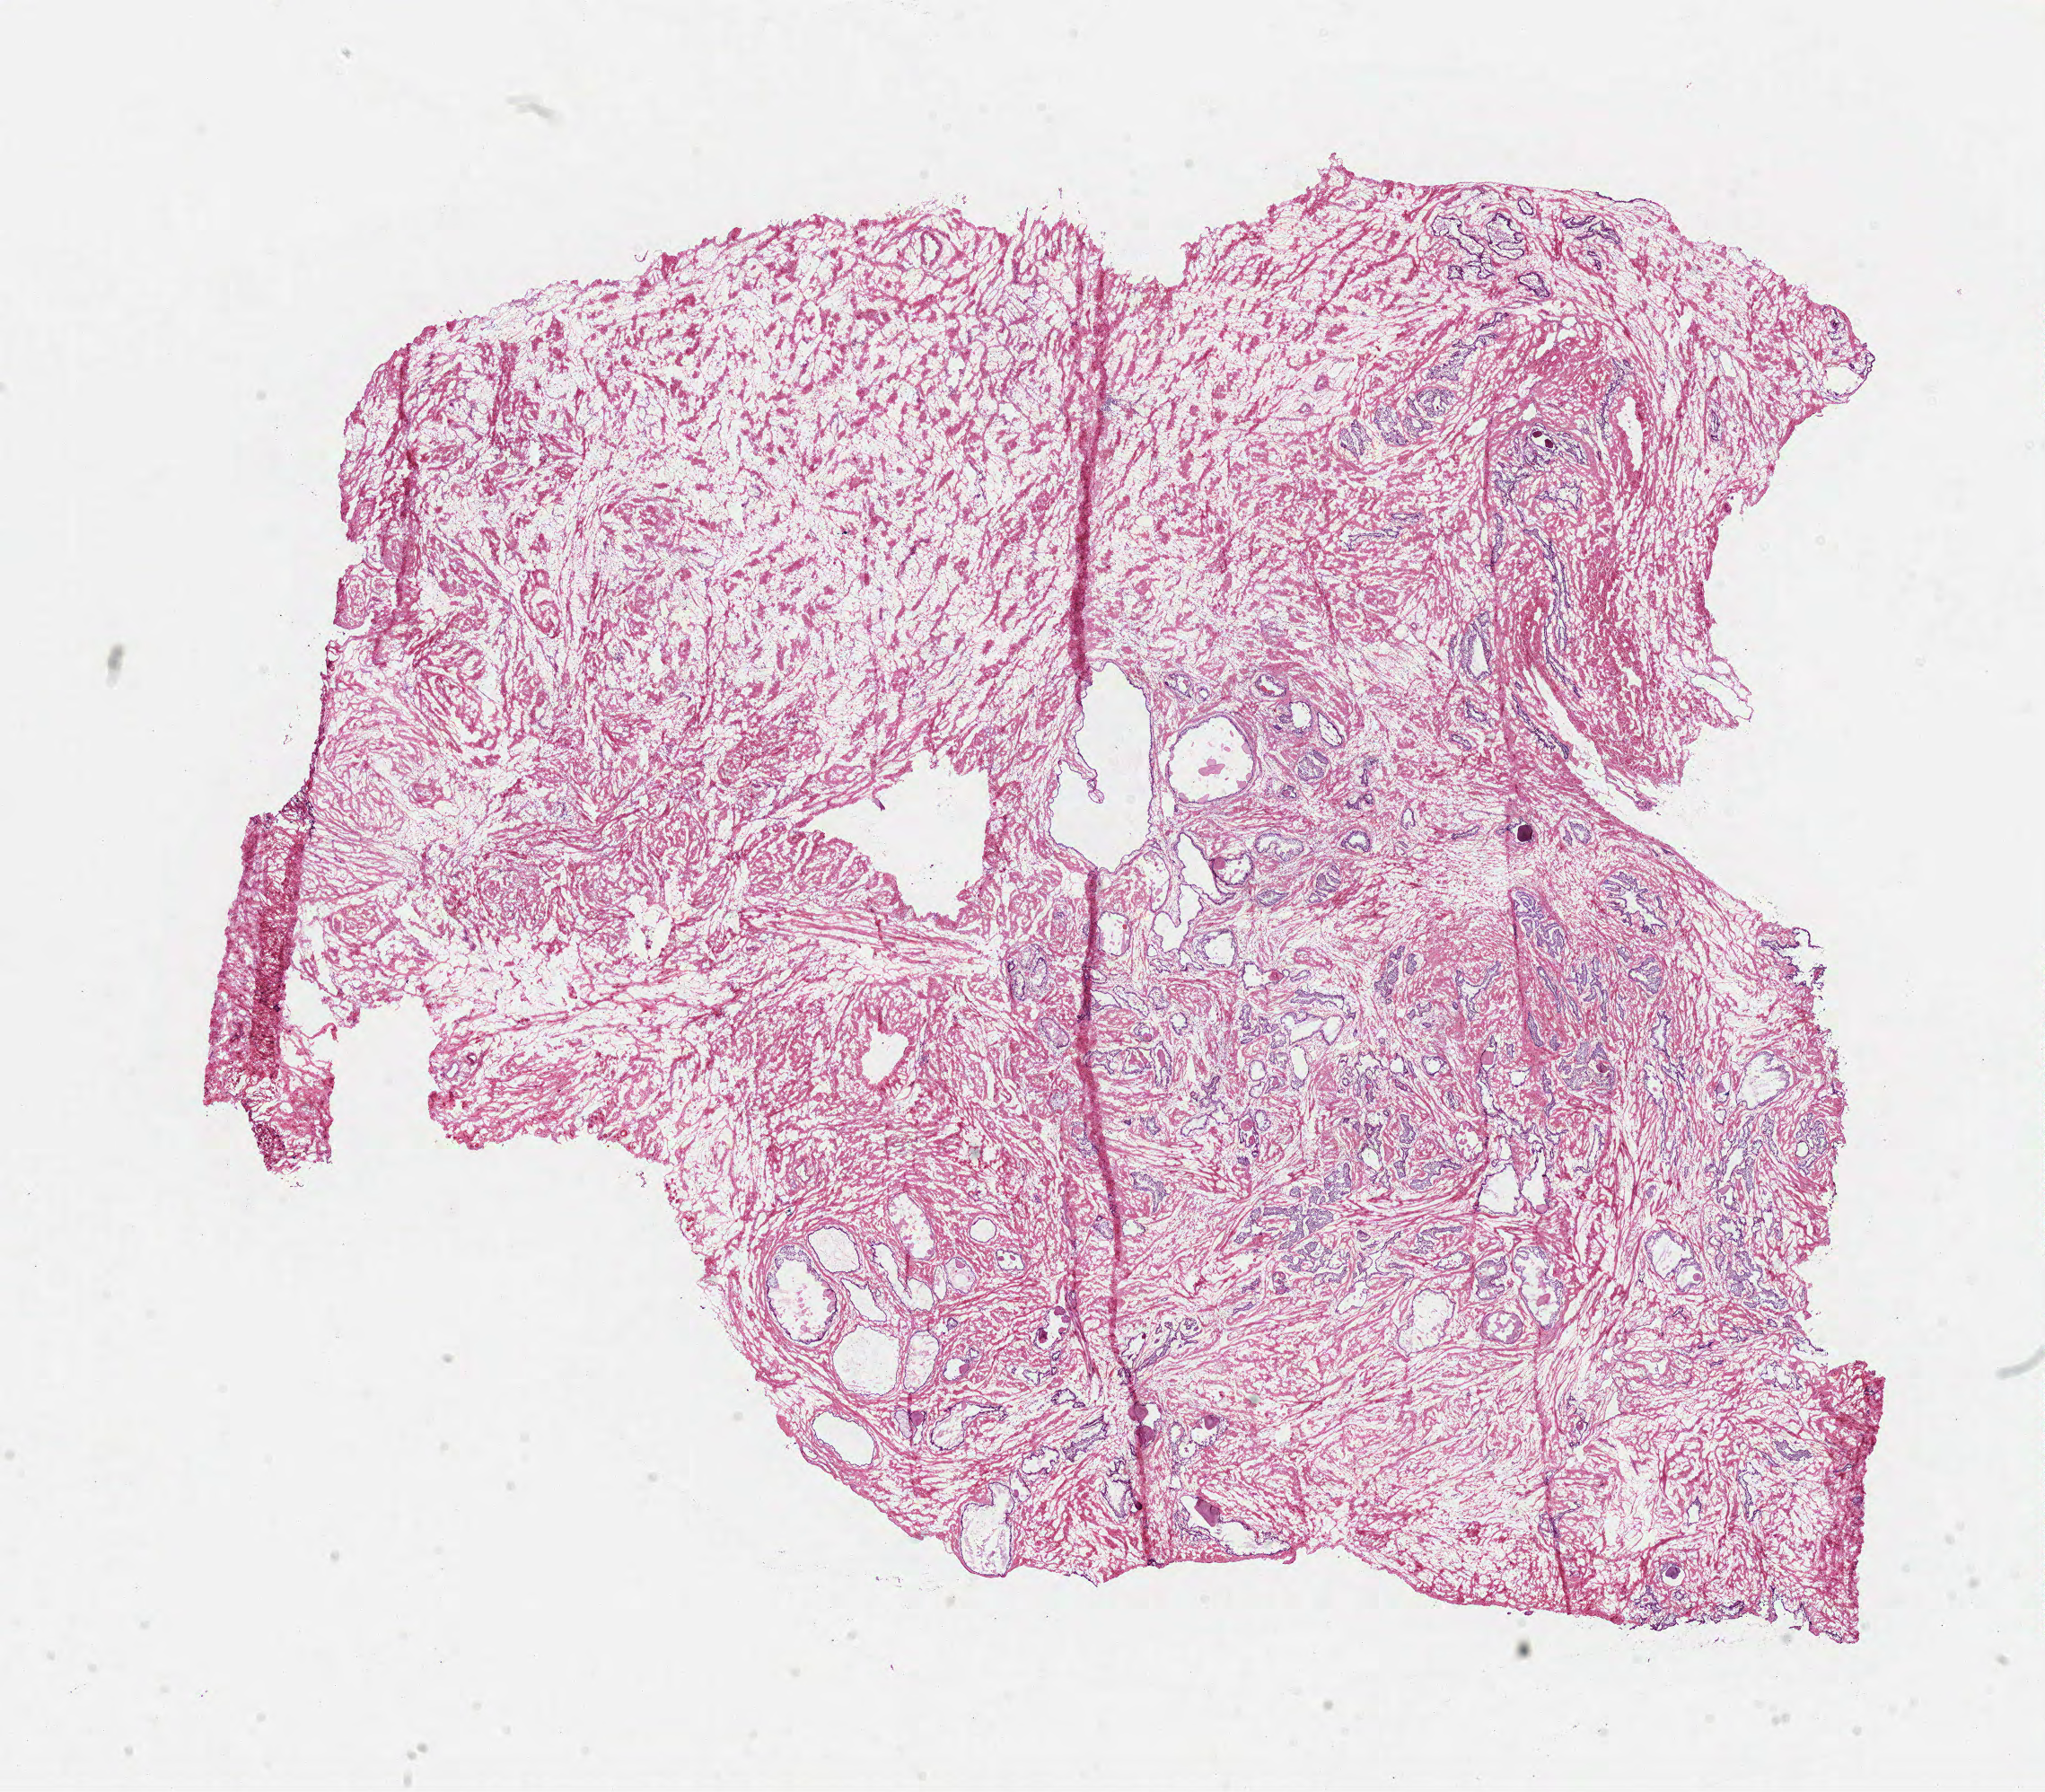
Hematoxylin and eosin (H&E) stained whole-slide image, shown as a low-resolution overview of the whole scanned area (about 18.4 x 16.1 mm). Frozen section from the top of the tissue portion. Prostate, solid tissue normal (non-tumour tissue) sample. Male, age 65 years at initial diagnosis.
This section: solid tissue normal (non-tumour) sample from the same patient. Patient diagnosis: Acinar cell carcinoma (prostate gland).